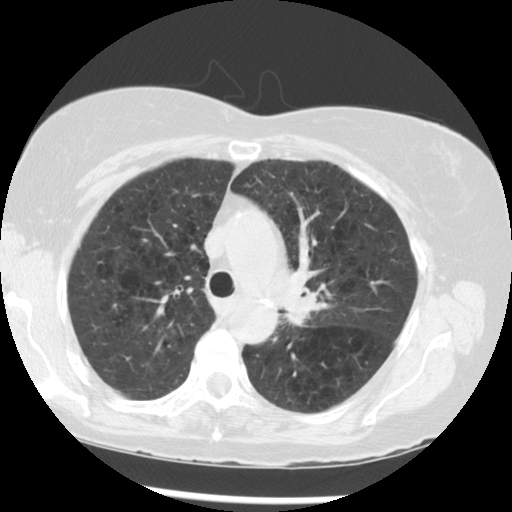
Low-dose screening chest CT, axial slice; third screening round (two years after baseline); lung window (W 1500 / L -600 HU); 2.5 mm slice thickness; standard (soft-tissue) reconstruction kernel (STANDARD); slice 207 of 283 in the series; 512 × 512 image matrix, field of view 330 × 330 mm. Female participant, aged 70 years at enrolment. Current smoker at enrolment.
Expert reader's lesion annotation, bounding box [x1, y1, x2, y2] px = [271, 260, 364, 350]. The exam's reader record, not a measurement of the box and not confirmed to be the same lesion: non-calcified nodule or mass ≥4 mm, left upper lobe, 32 × 26 mm, spiculated (stellate) margins, soft tissue attenuation, pre-existing on the prior screen: yes; interval growth: yes. Official screen result: positive, other. Lung cancer was diagnosed 24 days after this screen: neoplasm, malignant, left upper lobe, stage IIIB (AJCC 6th edition), 40 mm at pathology.